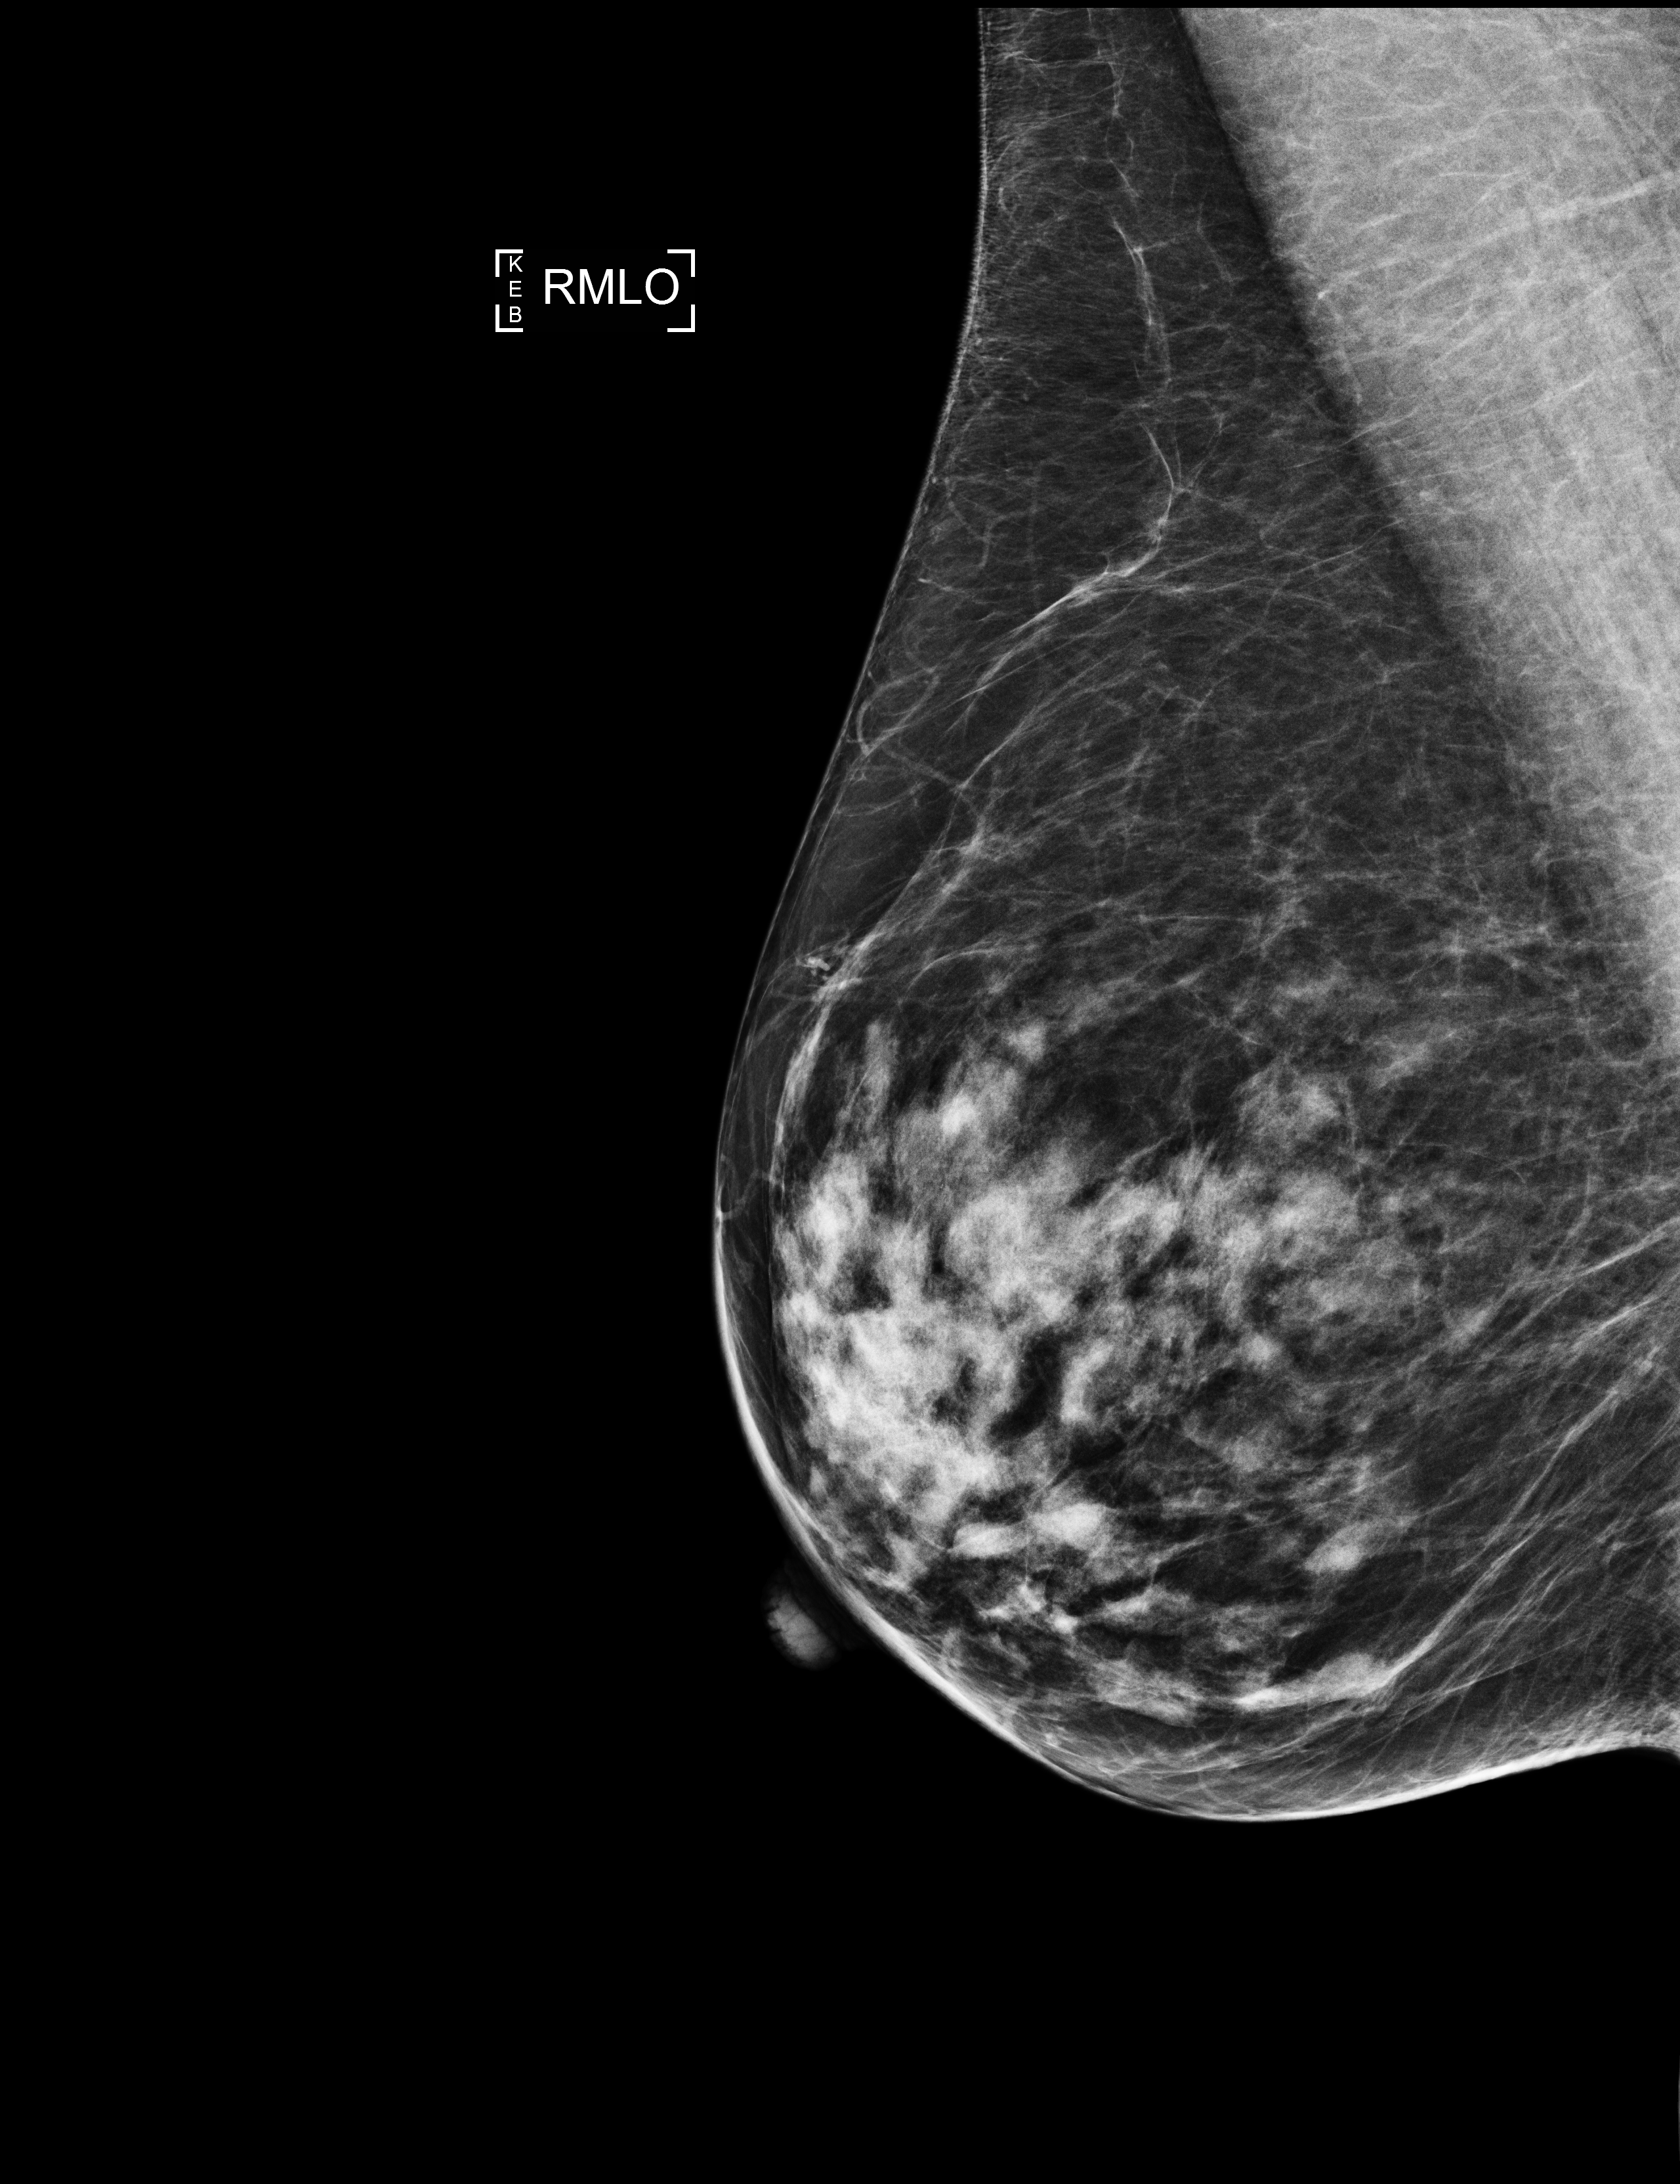
Screening examination, compressed breast thickness 56 mm. Patient aged 73 years (female).
Image type: full-field digital mammogram. Breast: right. Projection: mediolateral oblique (MLO) view.